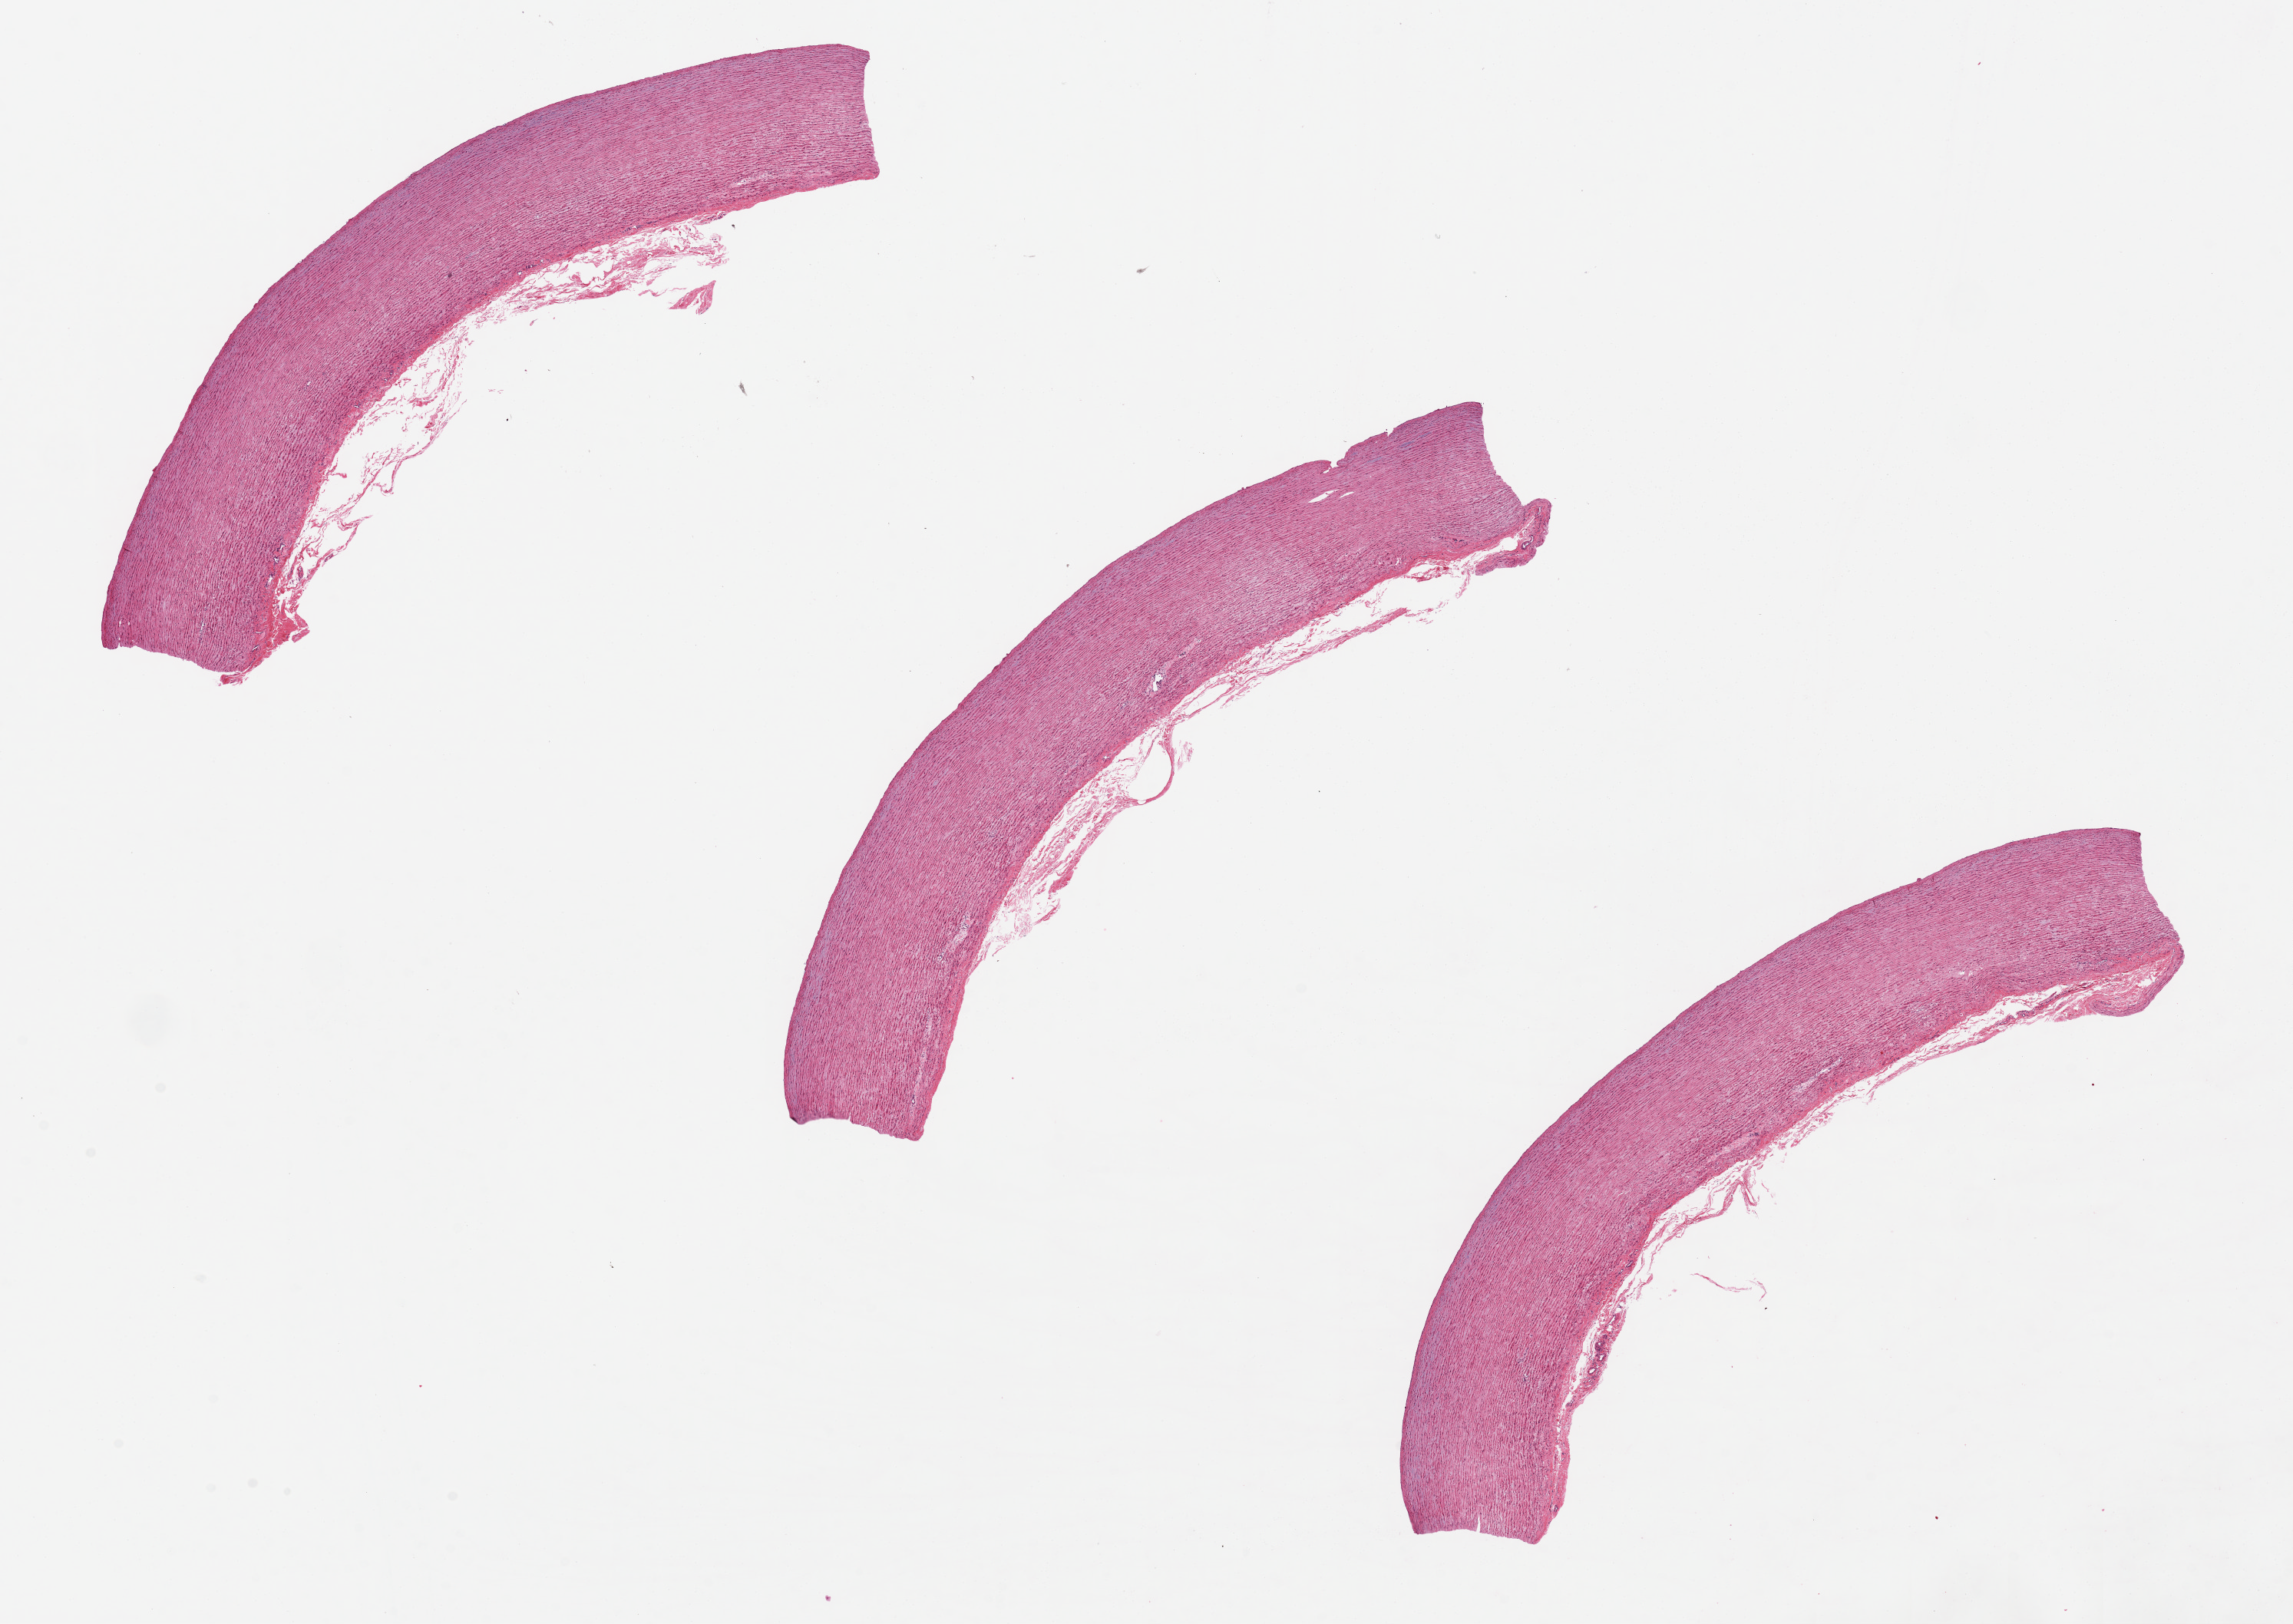
Whole-slide image, haematoxylin and eosin stain, brightfield, a low-resolution overview of the entire scanned area, about 23.6 x 16.7 mm (from a 20x scan); PAXgene-fixed paraffin-embedded (PFPE) section; section of aorta (target tissue); donor tissue sample. Male donor.
* review note (as recorded): 1. 10x1.6mm. Clean specimen